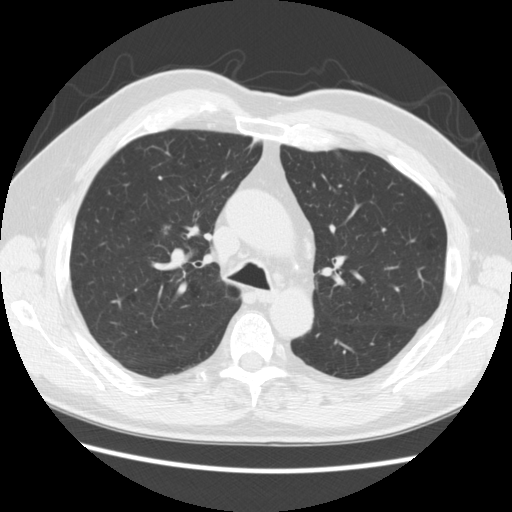
Low-dose screening chest CT, one axial slice; slice 173 of 259 in the series (ordered by position); reconstruction kernel STANDARD; 120 kVp; lung window (W 1500 / L -600 HU); 2.5 mm slice thickness; 512 × 512 image matrix, field of view 360 × 360 mm.
Structures marked on this image (outlined manually by an expert reader):
- lesion 1 (tumor, upper lobe of right lung): bounding box (x1, y1, x2, y2) in pixels: (165, 227, 169, 229)